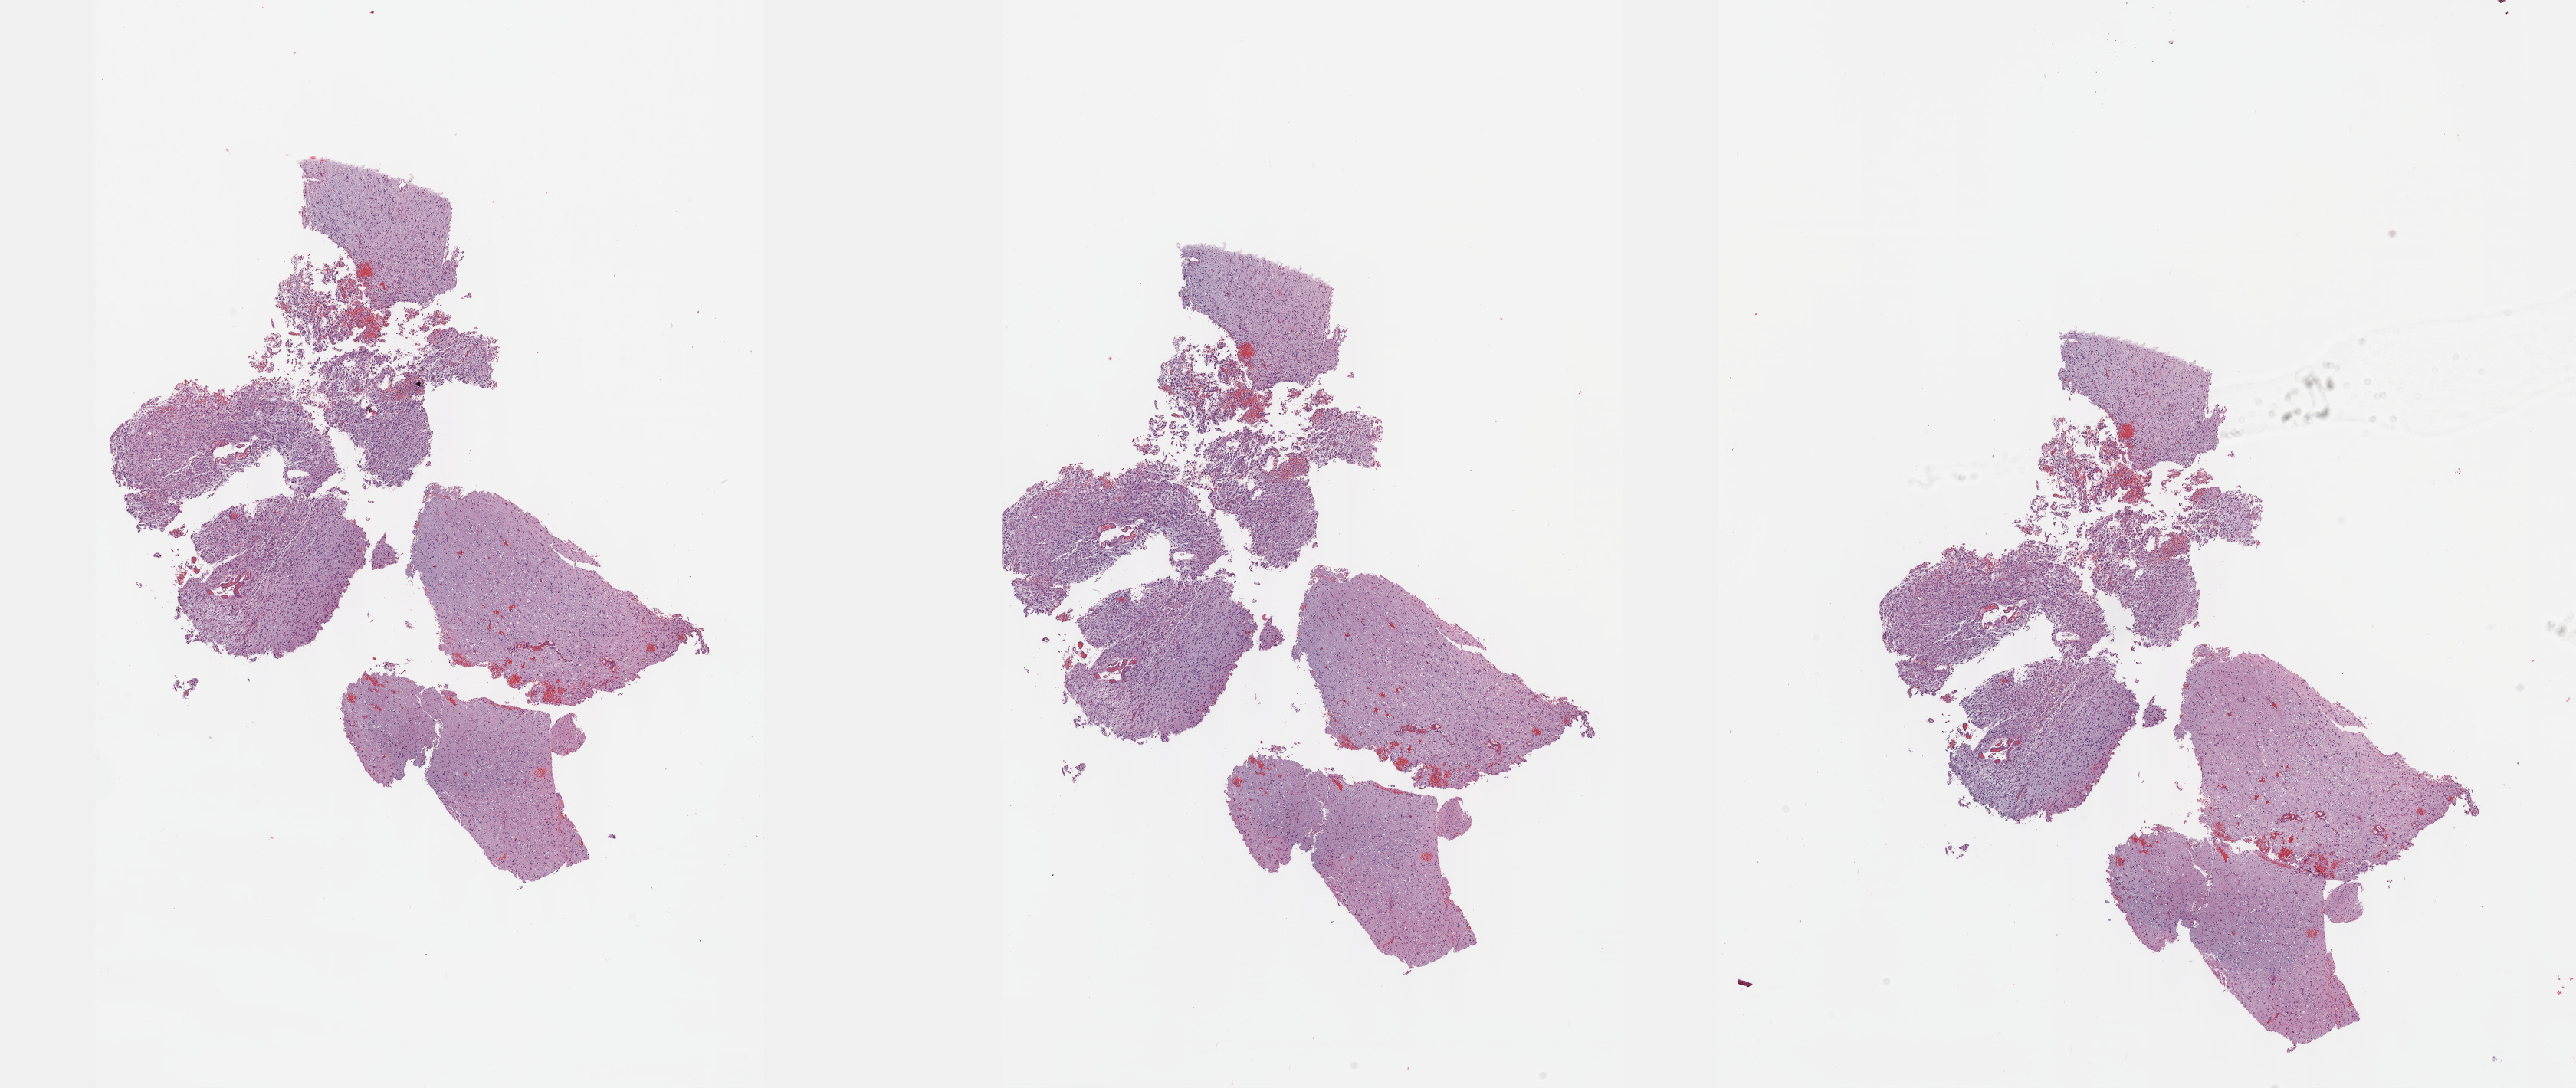
Digitized H&E tissue section (whole slide), whole scanned area (about 27.2 x 11.5 mm, slide scanned at 40x) shown as a low-resolution overview; FFPE section; primary tumour sample from the brain. Female, age 41 years at initial diagnosis. Histologic grade: G3 (poorly differentiated).
Pathologic diagnosis: Oligodendroglioma, anaplastic (cerebrum).